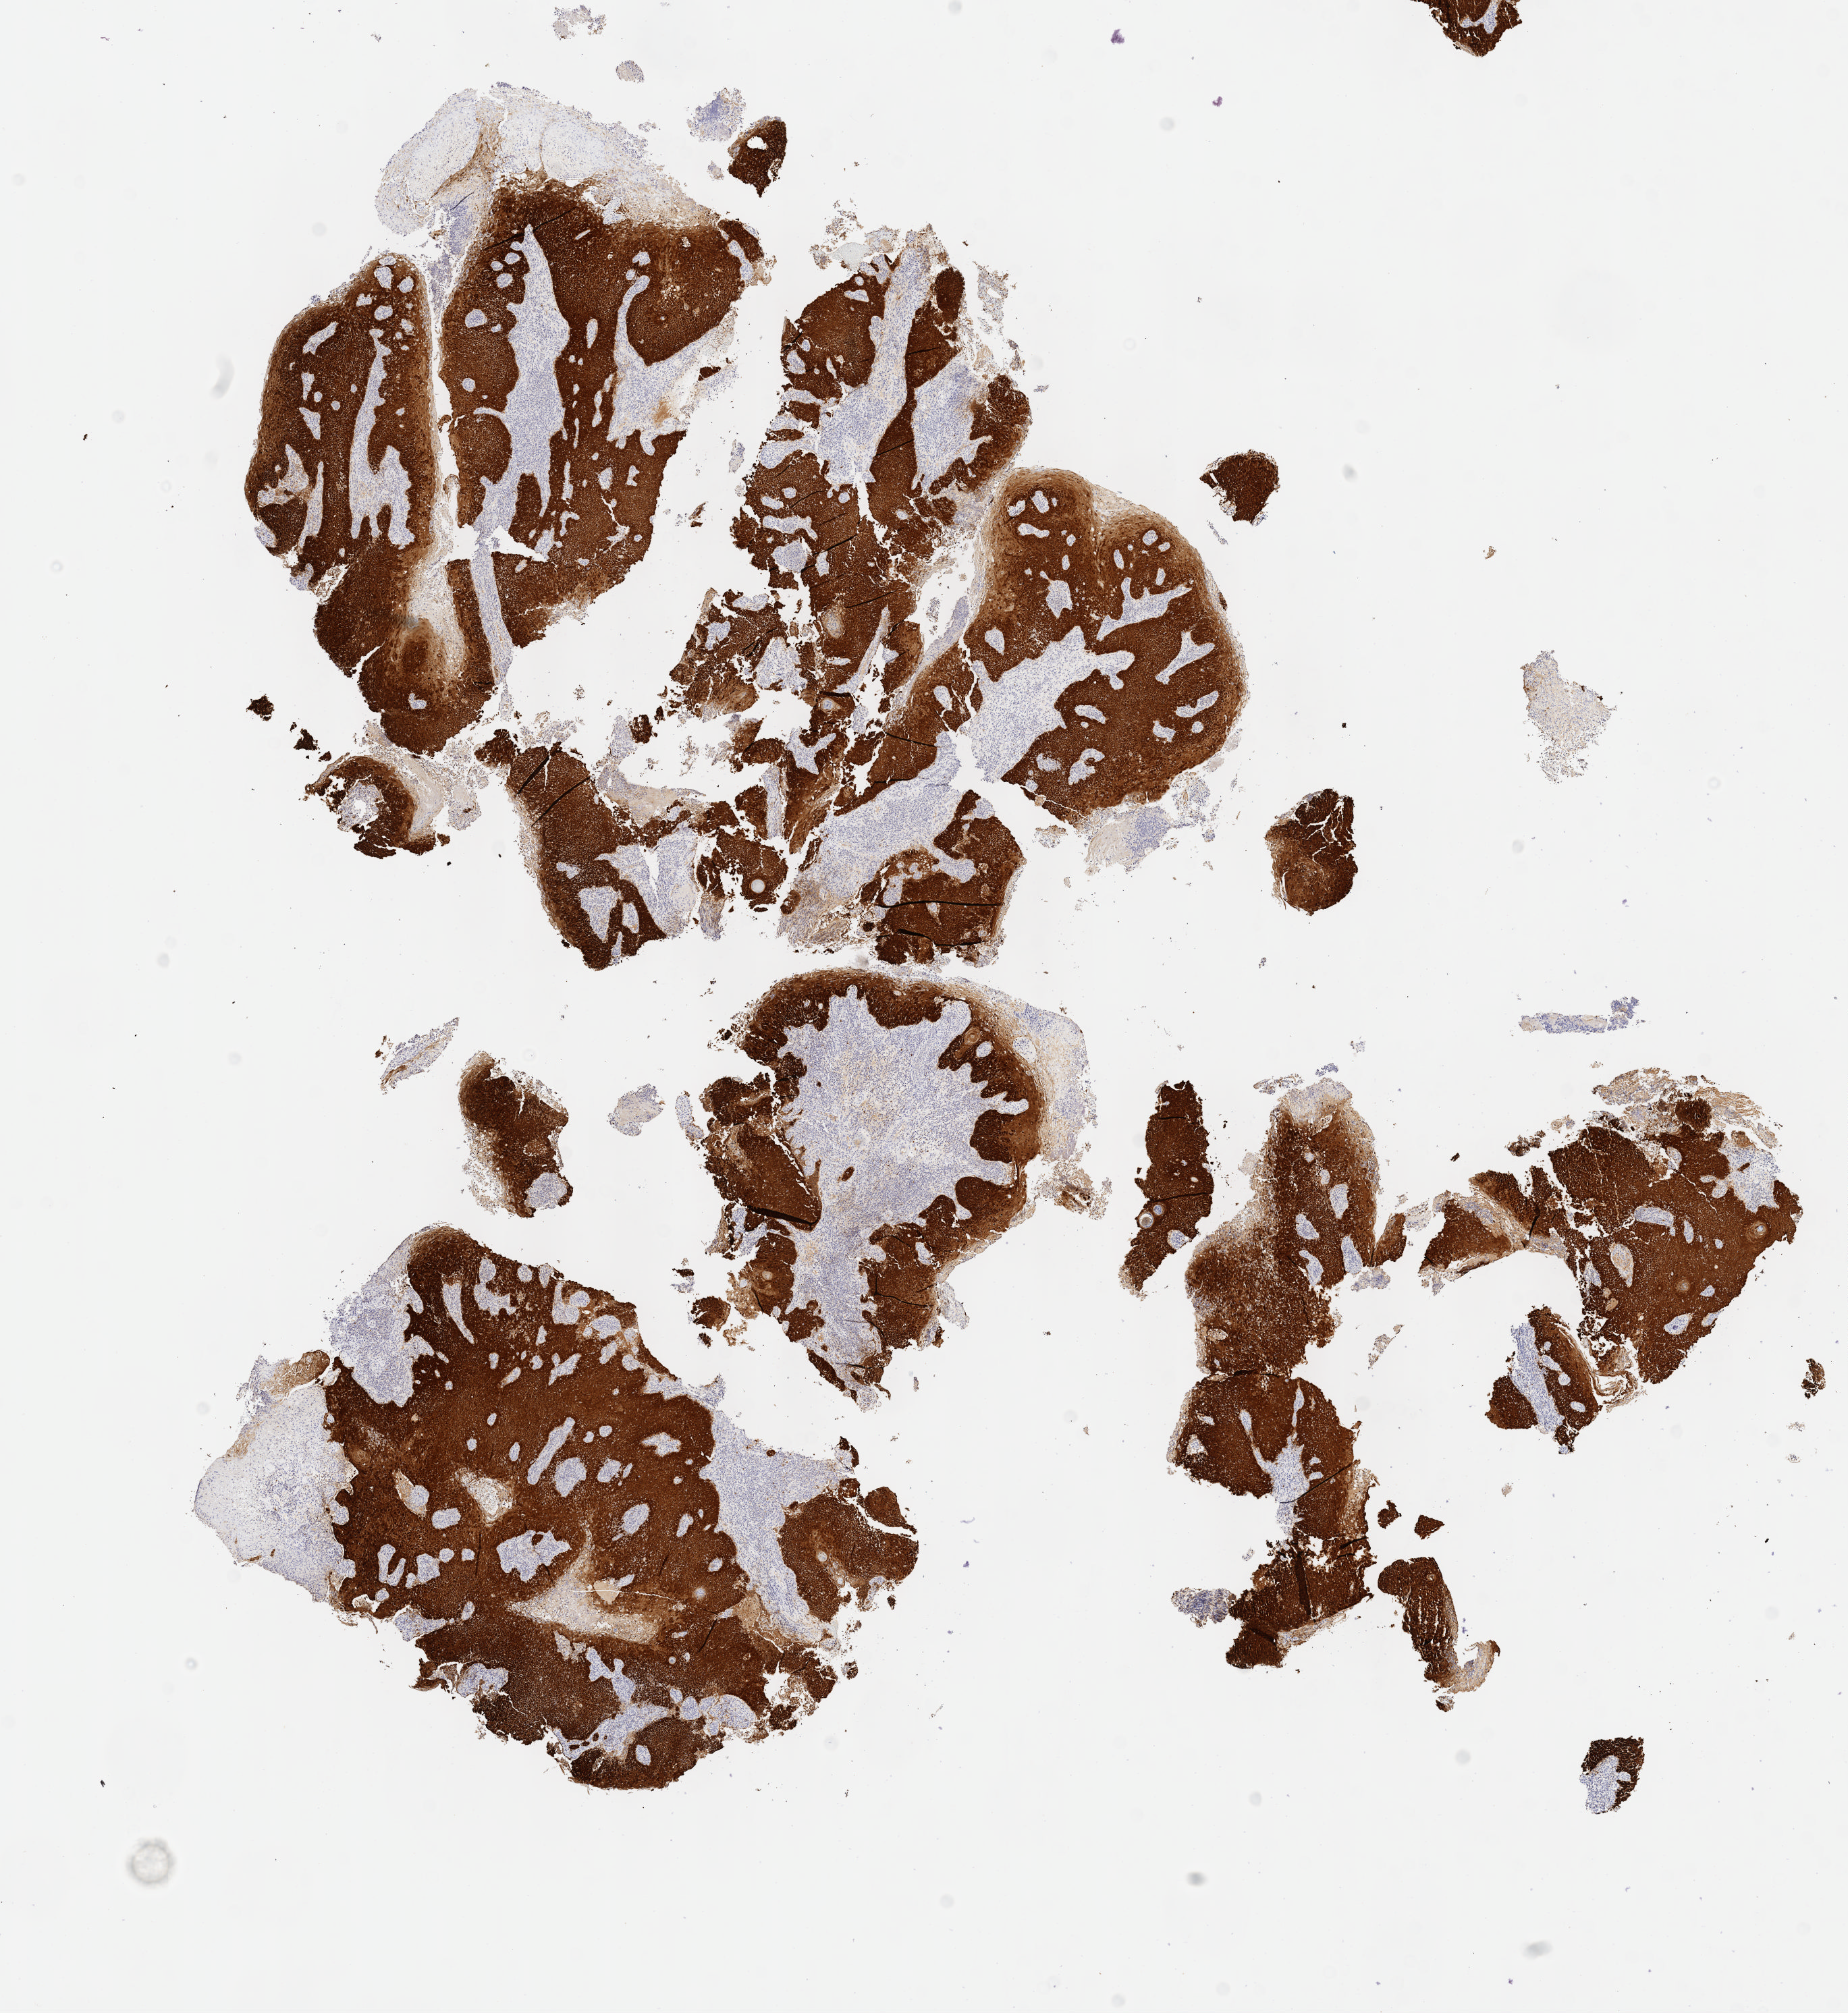
Immunohistochemistry (IHC) whole-slide image stained for p16 (p16INK4a), a low-resolution overview of the entire scanned area, about 11.1 x 12.1 mm; specimen: tumor tissue; site: cervix. Patient female; 45 years old.
Diagnosis: Squamous cell carcinoma, large cell, nonkeratinizing, NOS.